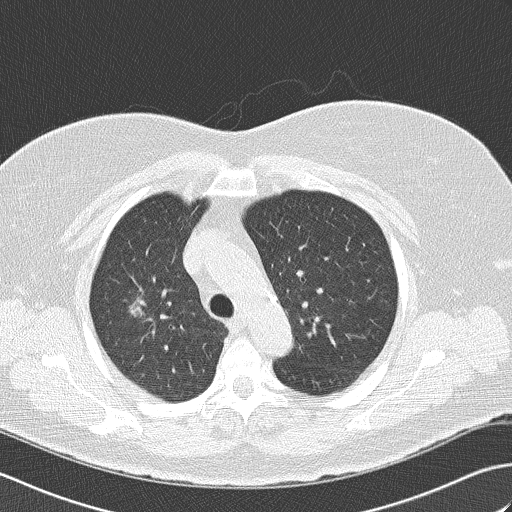
Chest CT (low-dose screening protocol), one axial image. Second screening round (one year after baseline). Lung window (W 1500 / L -600 HU). Lung (sharp) reconstruction kernel (B50f). Slice 115 of 148 in the series. 512 × 512 image matrix, field of view 350 × 350 mm. Female, age 74 years at enrolment. Former smoker at enrolment.
• Expert-annotated lung lesion, bounding box [x1, y1, x2, y2] px = [104, 280, 168, 334].
• The screening reader recorded 4 non-calcified nodules or masses ≥4 mm on this exam; which of them this box marks is not recorded.
• Lung cancer was diagnosed 453 days after this screen: bronchiolo-alveolar carcinoma, non-mucinous, right upper lobe, well differentiated (G1), stage IA (AJCC 6th edition), 14 mm at pathology.